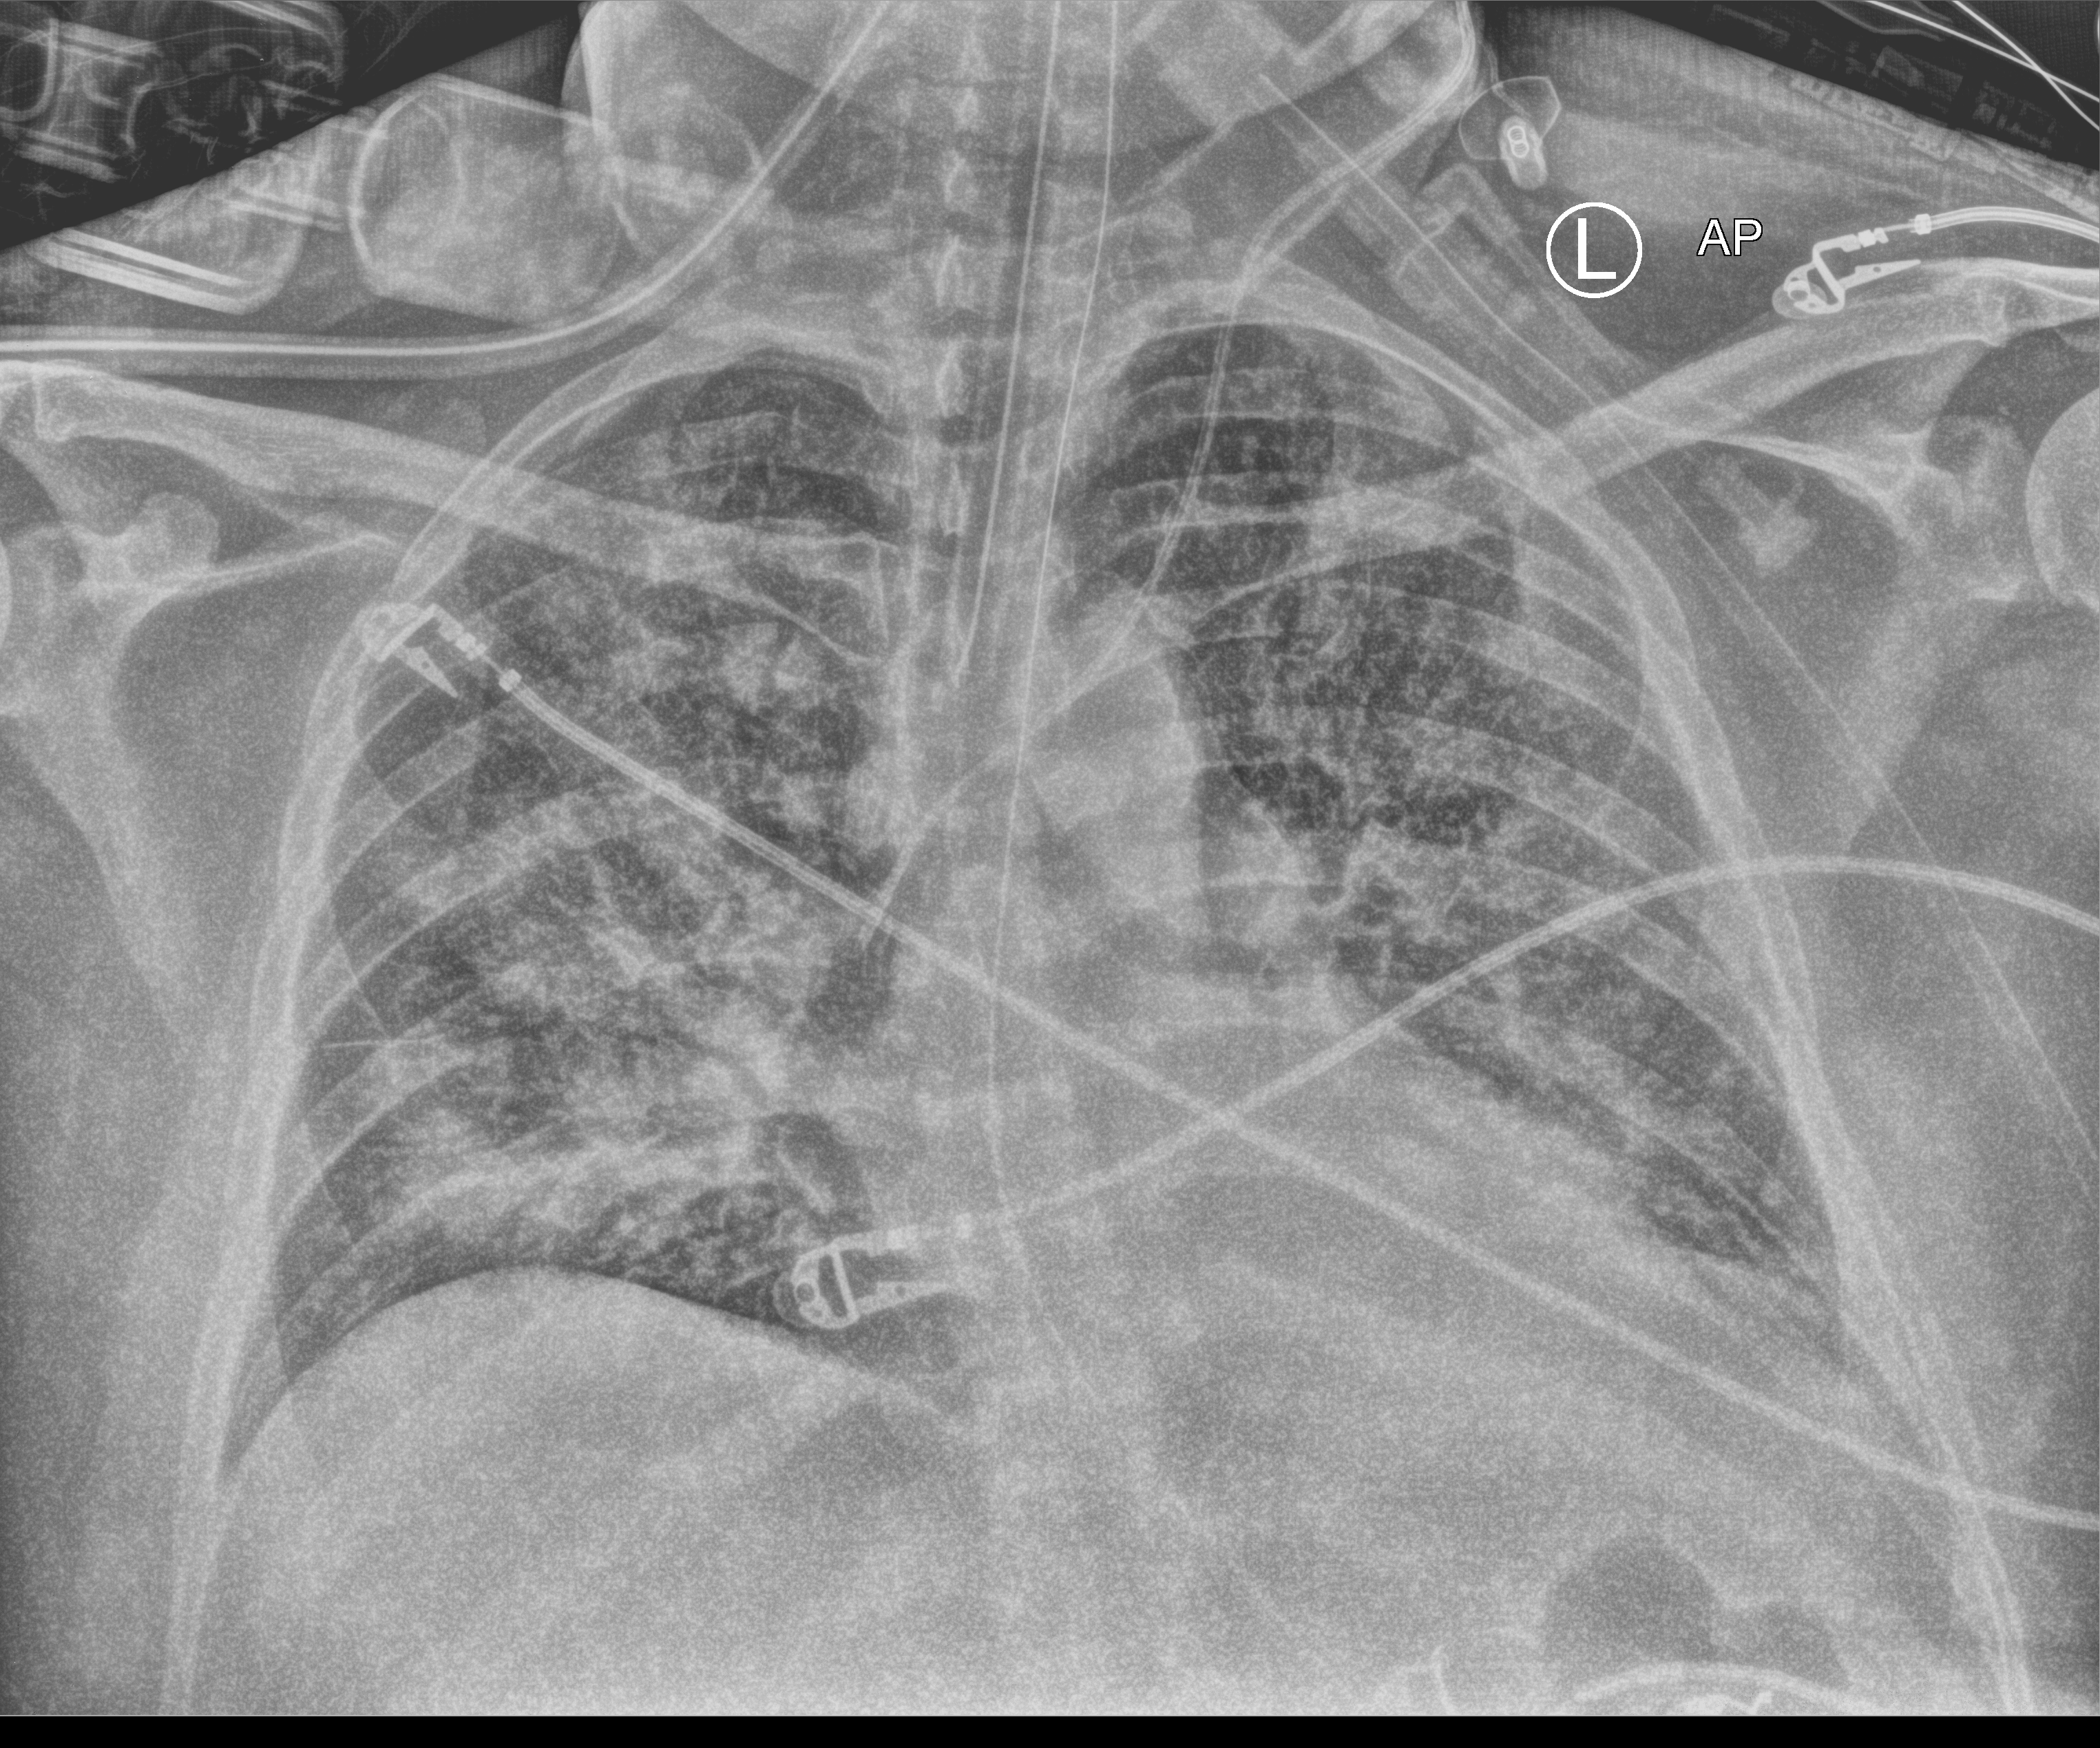
Portable chest radiograph. Patient hospitalised with COVID-19, aged 18–59 years.
Hospital-stay facts (about this admission, not read from this image; timing relative to this image not recorded):
- admitted to intensive care during this hospital stay: yes